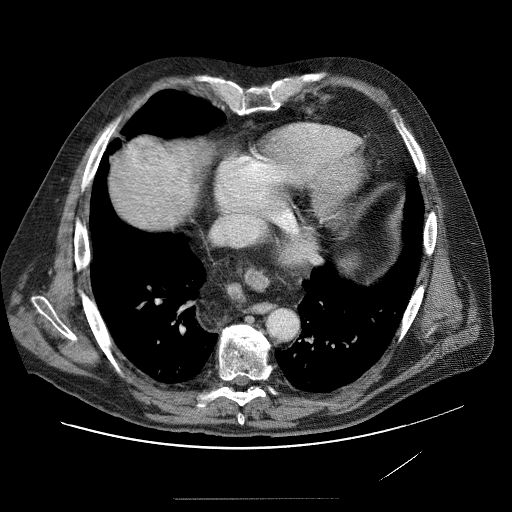
Contrast-enhanced abdominal CT (liver protocol), one axial slice. Position 79 of 89 along the scan axis. Reconstruction kernel STANDARD. Soft-tissue window (W 400 / L 40 HU). 2.5 mm slice thickness. 512 × 512 image matrix, field of view 420 × 420 mm. Case-level facts recorded for this patient, not image findings: diagnosis: hepatocellular carcinoma (patient treated with transarterial chemoembolisation; whether this scan precedes or follows treatment is not stated here); TNM stage (as recorded): Stage-IVA; Child-Pugh class: A; tumour nodularity: multinodular.
Structures marked on this image (semi-automatically segmented with operator editing):
- liver parenchyma outside the tumour (the mass and vessels are separate outlines, so this box may not span the whole liver): bounding box (x1, y1, x2, y2) in pixels: (120, 140, 184, 212)
- mass: (135, 145, 180, 191)